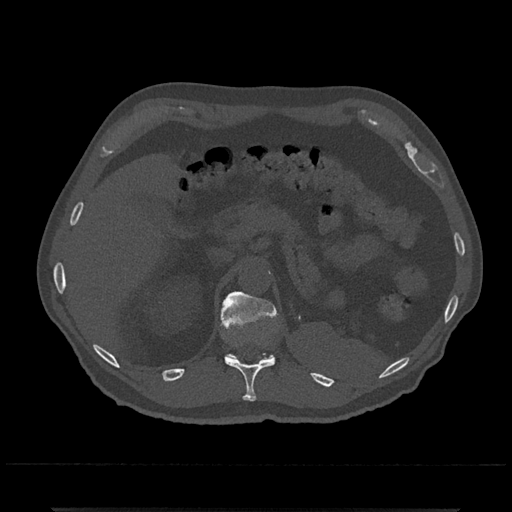
CT including the spine, one axial slice. Slice 467 of 797 in the series (ordered by position). 120 kVp. Bone window (W 1800 / L 400 HU). 0.5 mm slice thickness. 512 × 512 image matrix. Patient: male, 67 years. Case-level facts recorded for this patient, not image findings: primary cancer: prostate.
Structures marked on this image (semi-automatically segmented with operator editing):
- T11 vertebra: box from (x=225, y=336) to (x=276, y=402) px
- T12 vertebra: (x=221, y=291)–(x=279, y=360)